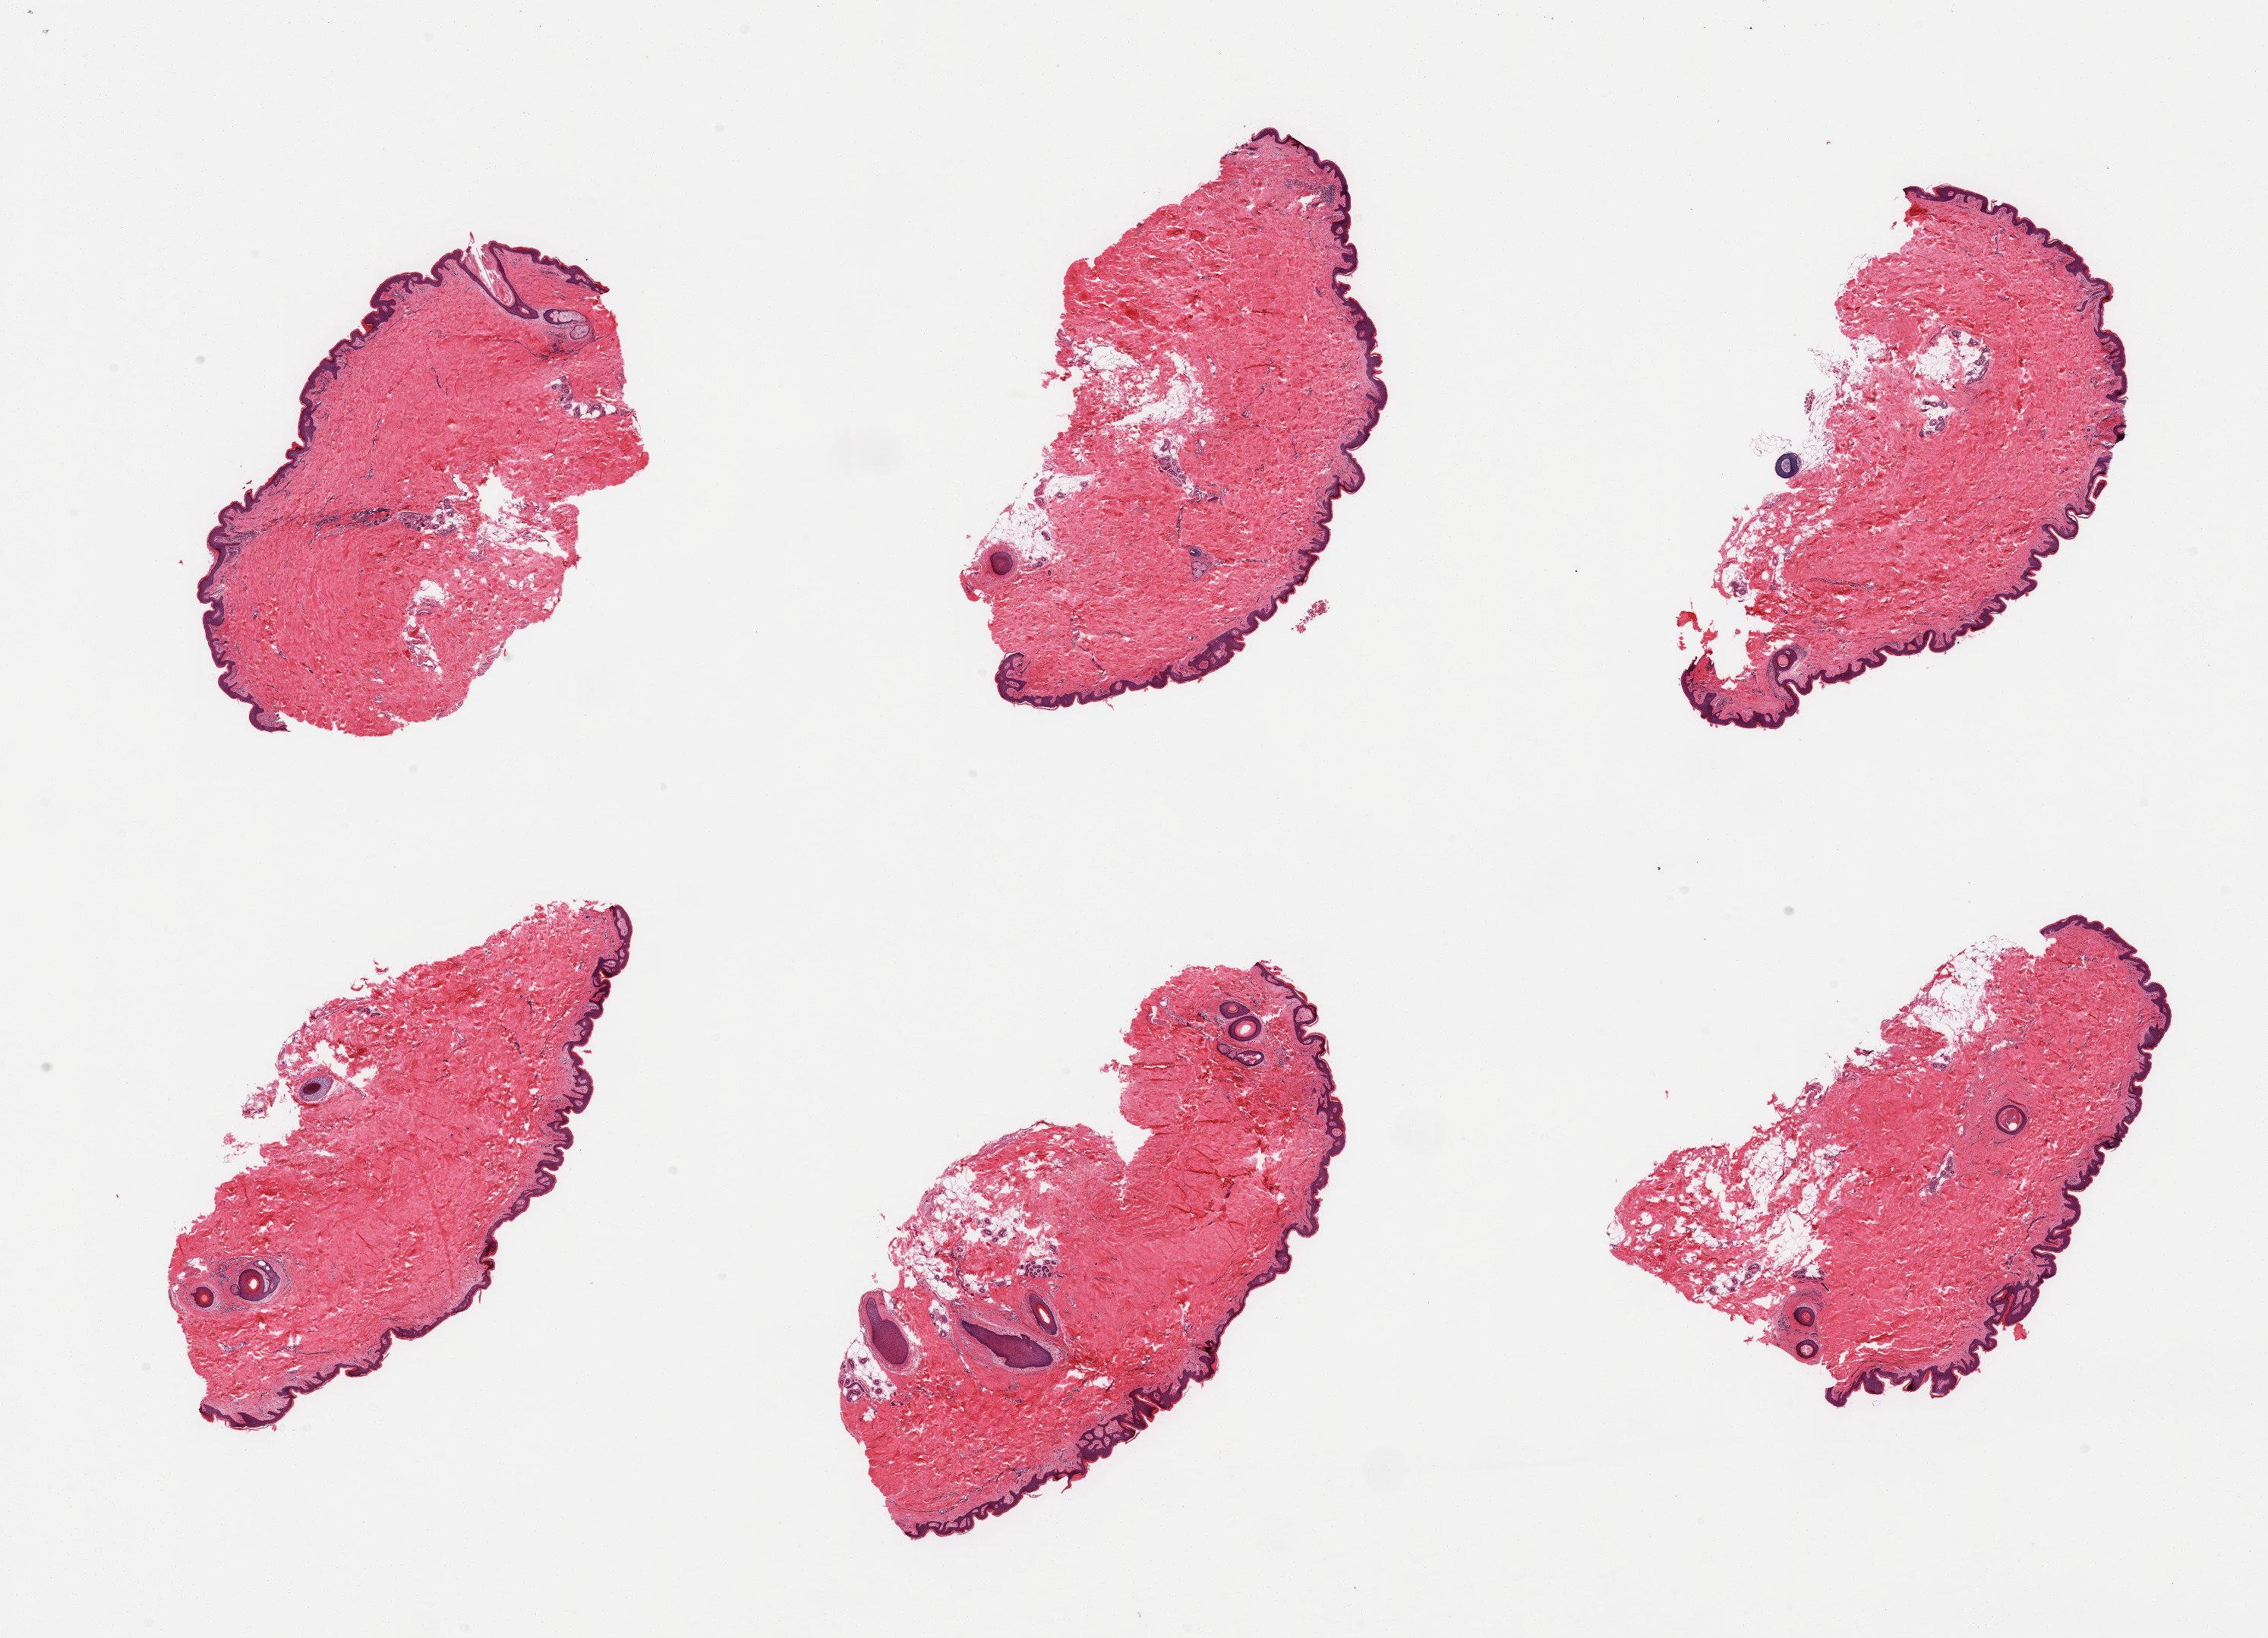
Haematoxylin and eosin whole-slide image, a low-resolution overview of the entire scanned area, about 23.6 x 17.1 mm (acquisition: 20x scan), PAXgene-fixed paraffin-embedded (PFPE) section, sampled site (target tissue): skin of suprapubic region, tissue donor sample. Donor: male.
Review note (as recorded): 6 pieces, no significant dermal fat, squamou epithelium is 45-60-microns.